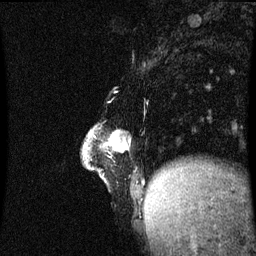
Breast MRI (dynamic contrast-enhanced), one sagittal slice; position 16 of 60 along the scan axis; dynamic contrast-enhanced series, image 2 of 3 at this slice position (ordered by acquisition); 1.5 T; TE 4.2 ms, TR 8.9 ms; 2 mm slice thickness; 256 × 256 image matrix. Female patient, age 47 years. Case-level facts recorded for this patient, not image findings: setting: breast cancer imaged before/during neoadjuvant chemotherapy; receptor status: HR-positive, HER2-negative.
Annotated regions visible in this slice (semi-automatically segmented with operator editing):
- analysis volume of interest (the breast-tissue region the enhancement analysis was run in; not a lesion): bounding box (x1, y1, x2, y2) in pixels: (84, 128, 146, 199)
- tumour enhancement mask (voxels above the 70 % enhancement threshold inside the analysis volume of interest): (113, 134, 129, 151)